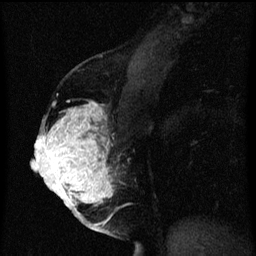
Breast MRI (dynamic contrast-enhanced), one sagittal slice; position 31 of 60 along the scan axis; dynamic contrast-enhanced series, image 2 of 3 at this slice position (ordered by acquisition); 1.5 T; TE 4.2 ms, TR 8 ms; 2 mm slice thickness; 256 × 256 image matrix, field of view 180 × 180 mm. Patient: female, 56 years.
Structures marked on this image (semi-automatically segmented with operator editing):
- analysis volume of interest (the breast-tissue region the enhancement analysis was run in; not a lesion): box from (x=40, y=104) to (x=121, y=209) px
- tumour enhancement mask (voxels above the 70 % enhancement threshold inside the analysis volume of interest): (x=40, y=104)–(x=113, y=209)